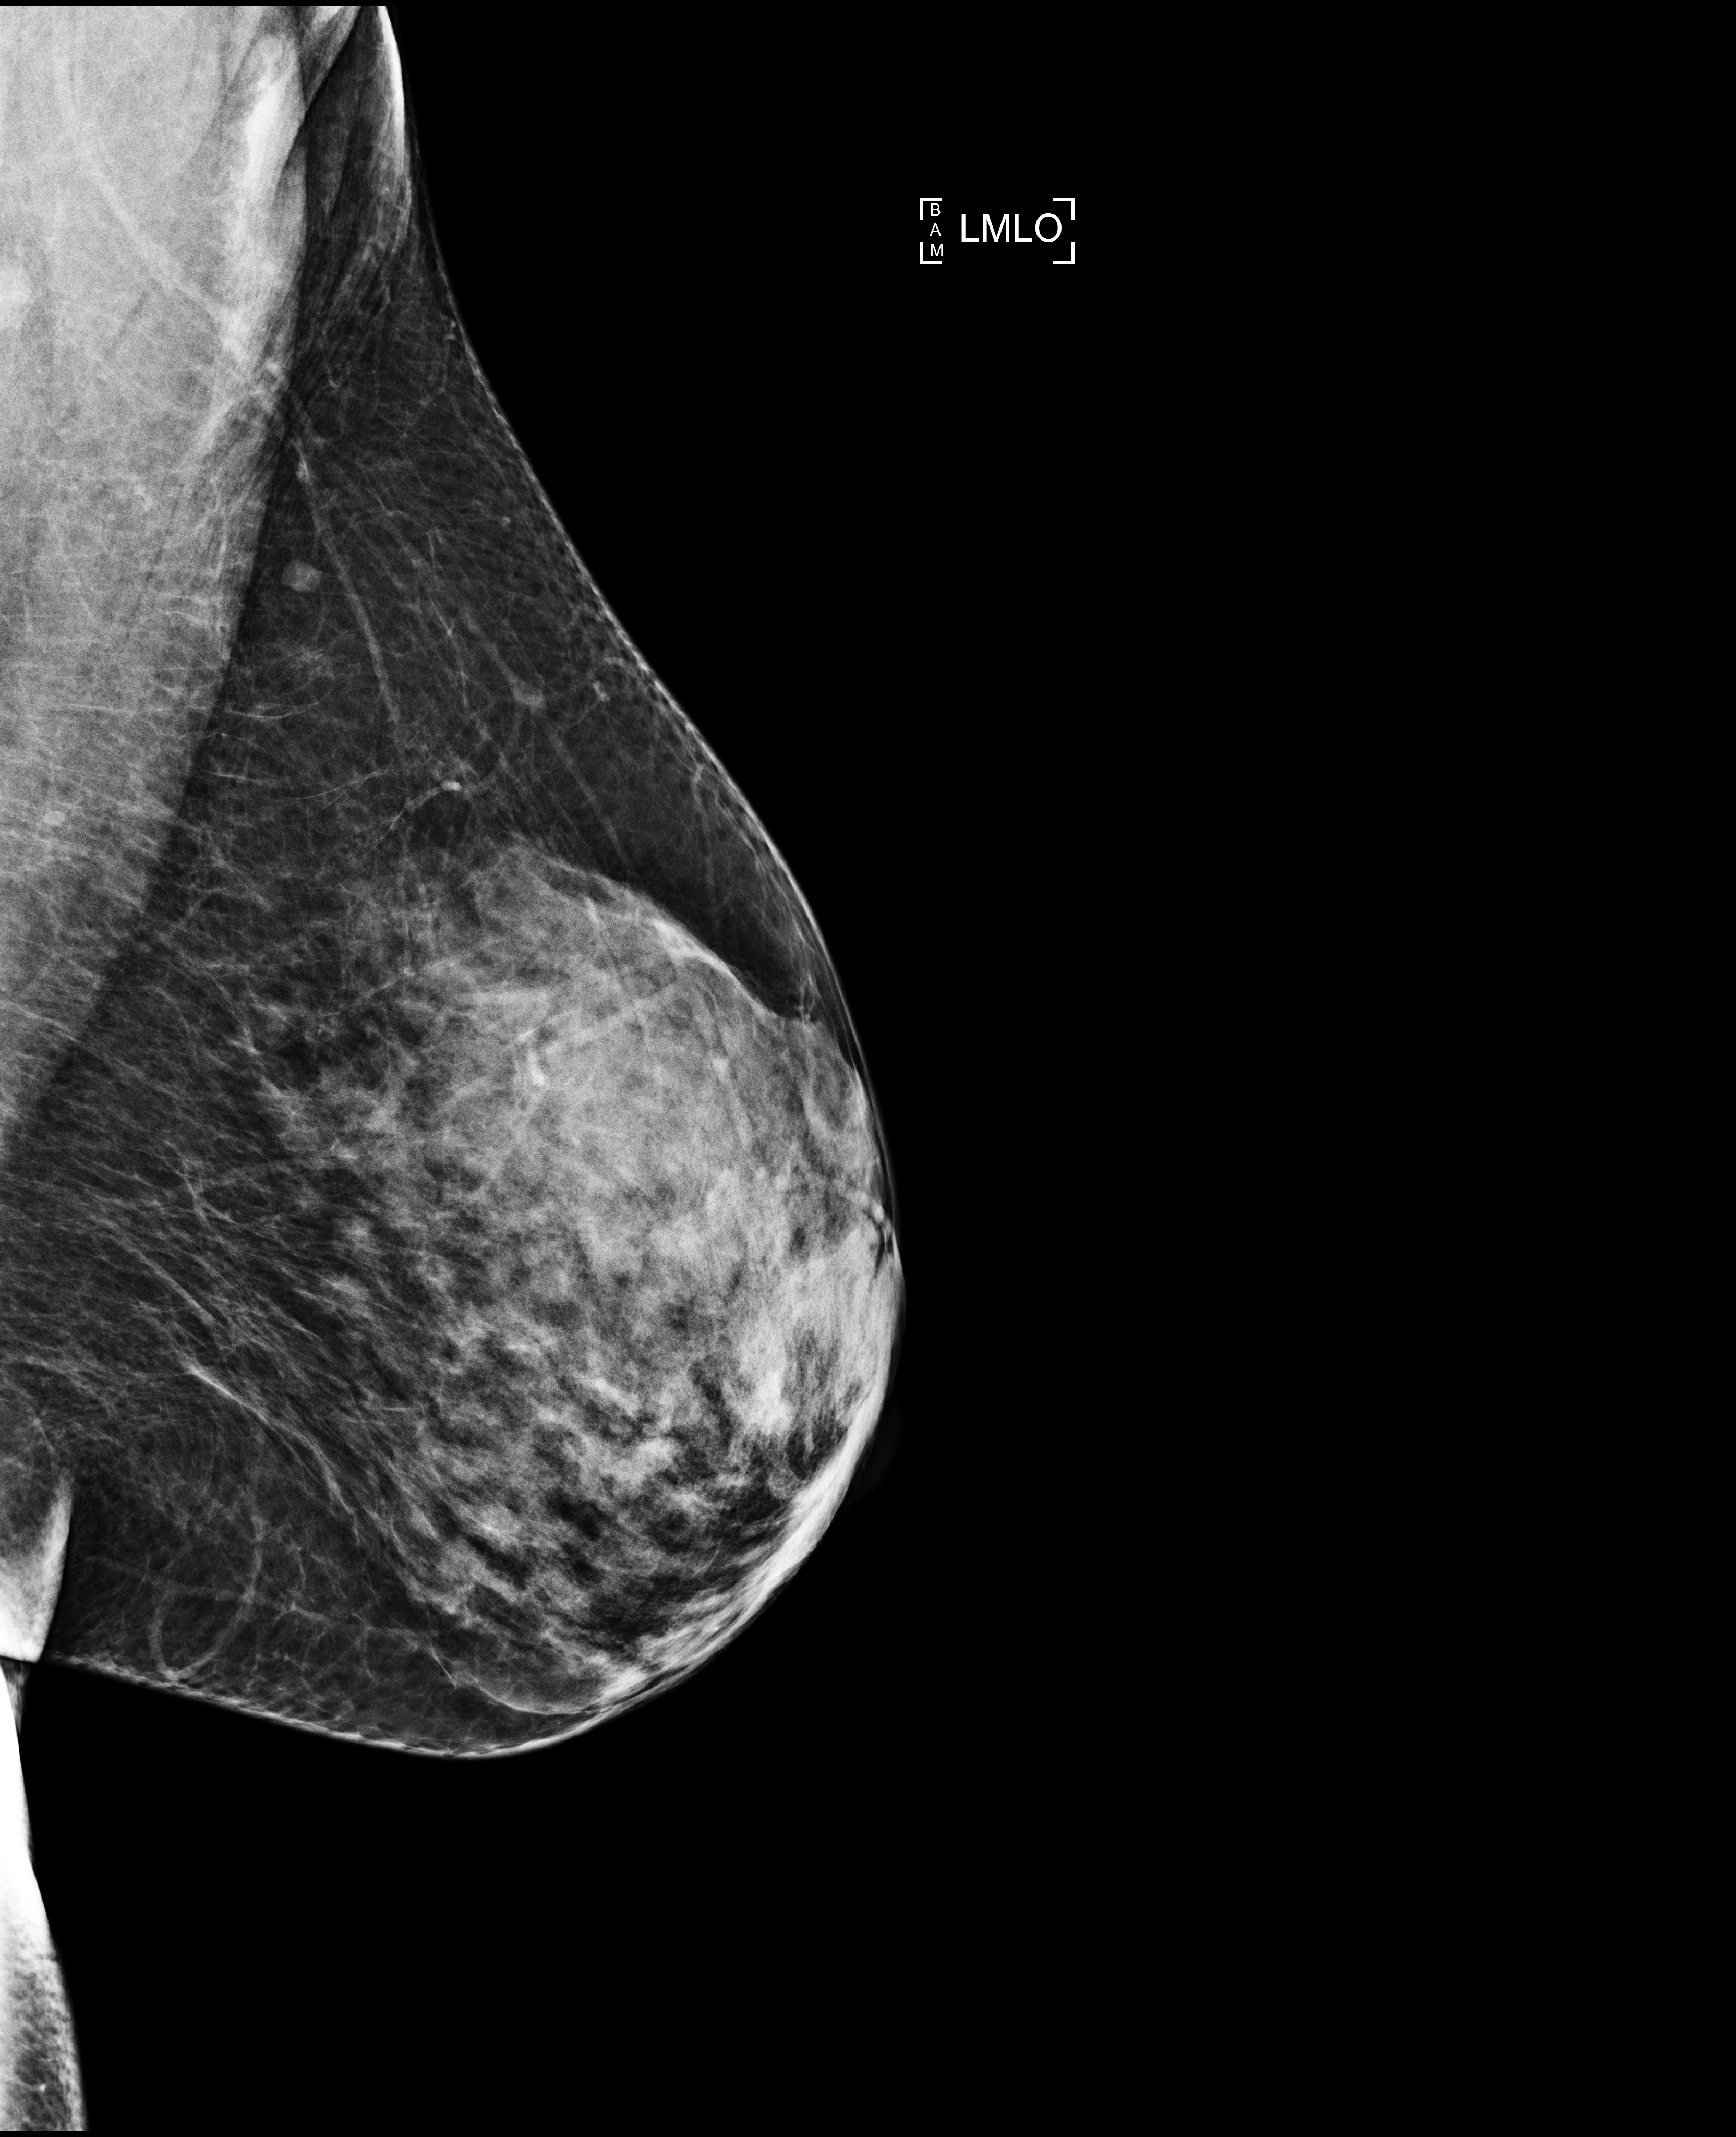
Annual screening mammography examination, compressed breast thickness 55 mm, system: Selenia Dimensions. Female patient, age 55 years.
Image type: full-field digital mammogram. Breast: left. Projection: medio-lateral oblique projection.